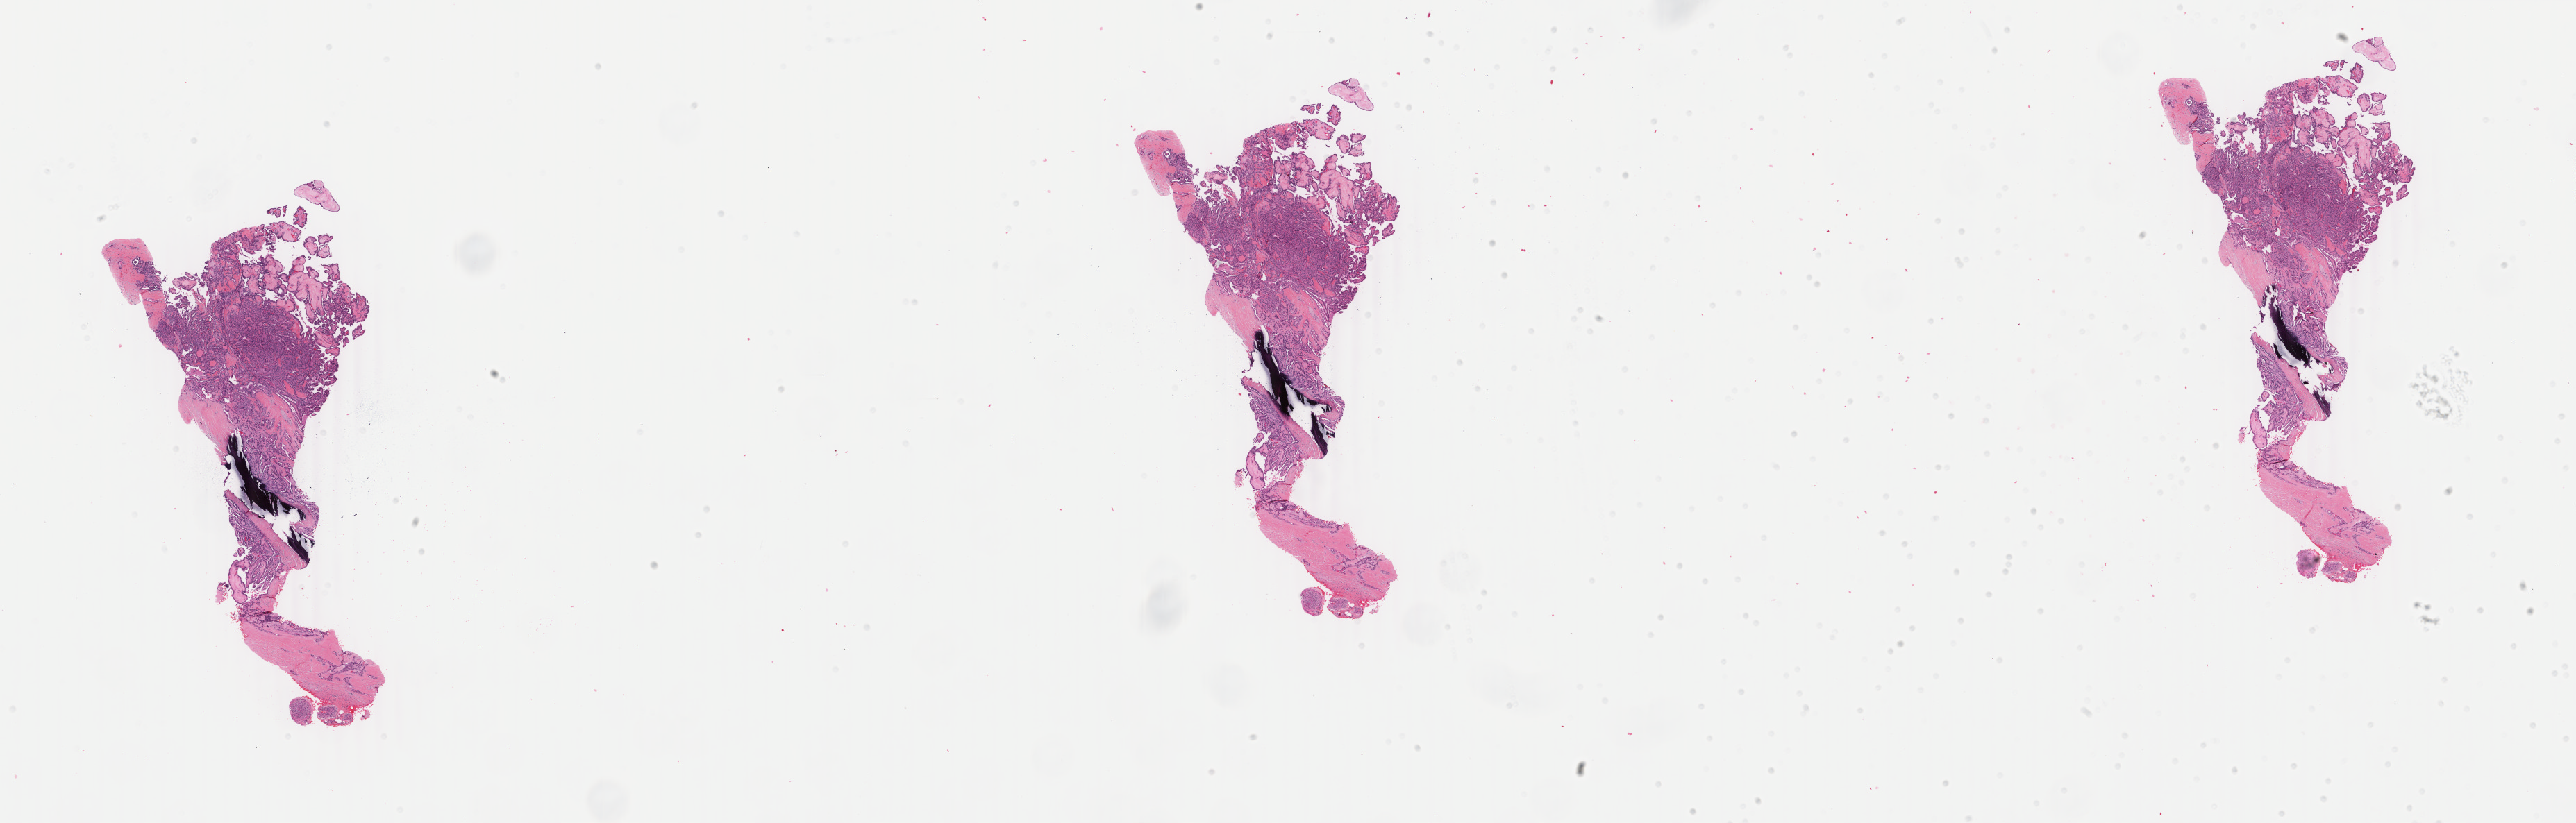
H&E whole-slide image — shown as a low-resolution overview of the whole scanned area (about 29.5 x 9.4 mm). Formalin-fixed paraffin-embedded (FFPE) diagnostic section. Primary tumour sample from the thyroid. Female patient; age at initial diagnosis 60 years.
Lymph nodes positive (case pathology): 4 of 22 examined. Diagnosis: Papillary adenocarcinoma, NOS. TNM: T4a N1b M1. AJCC pathologic stage: IVC (6th edition).